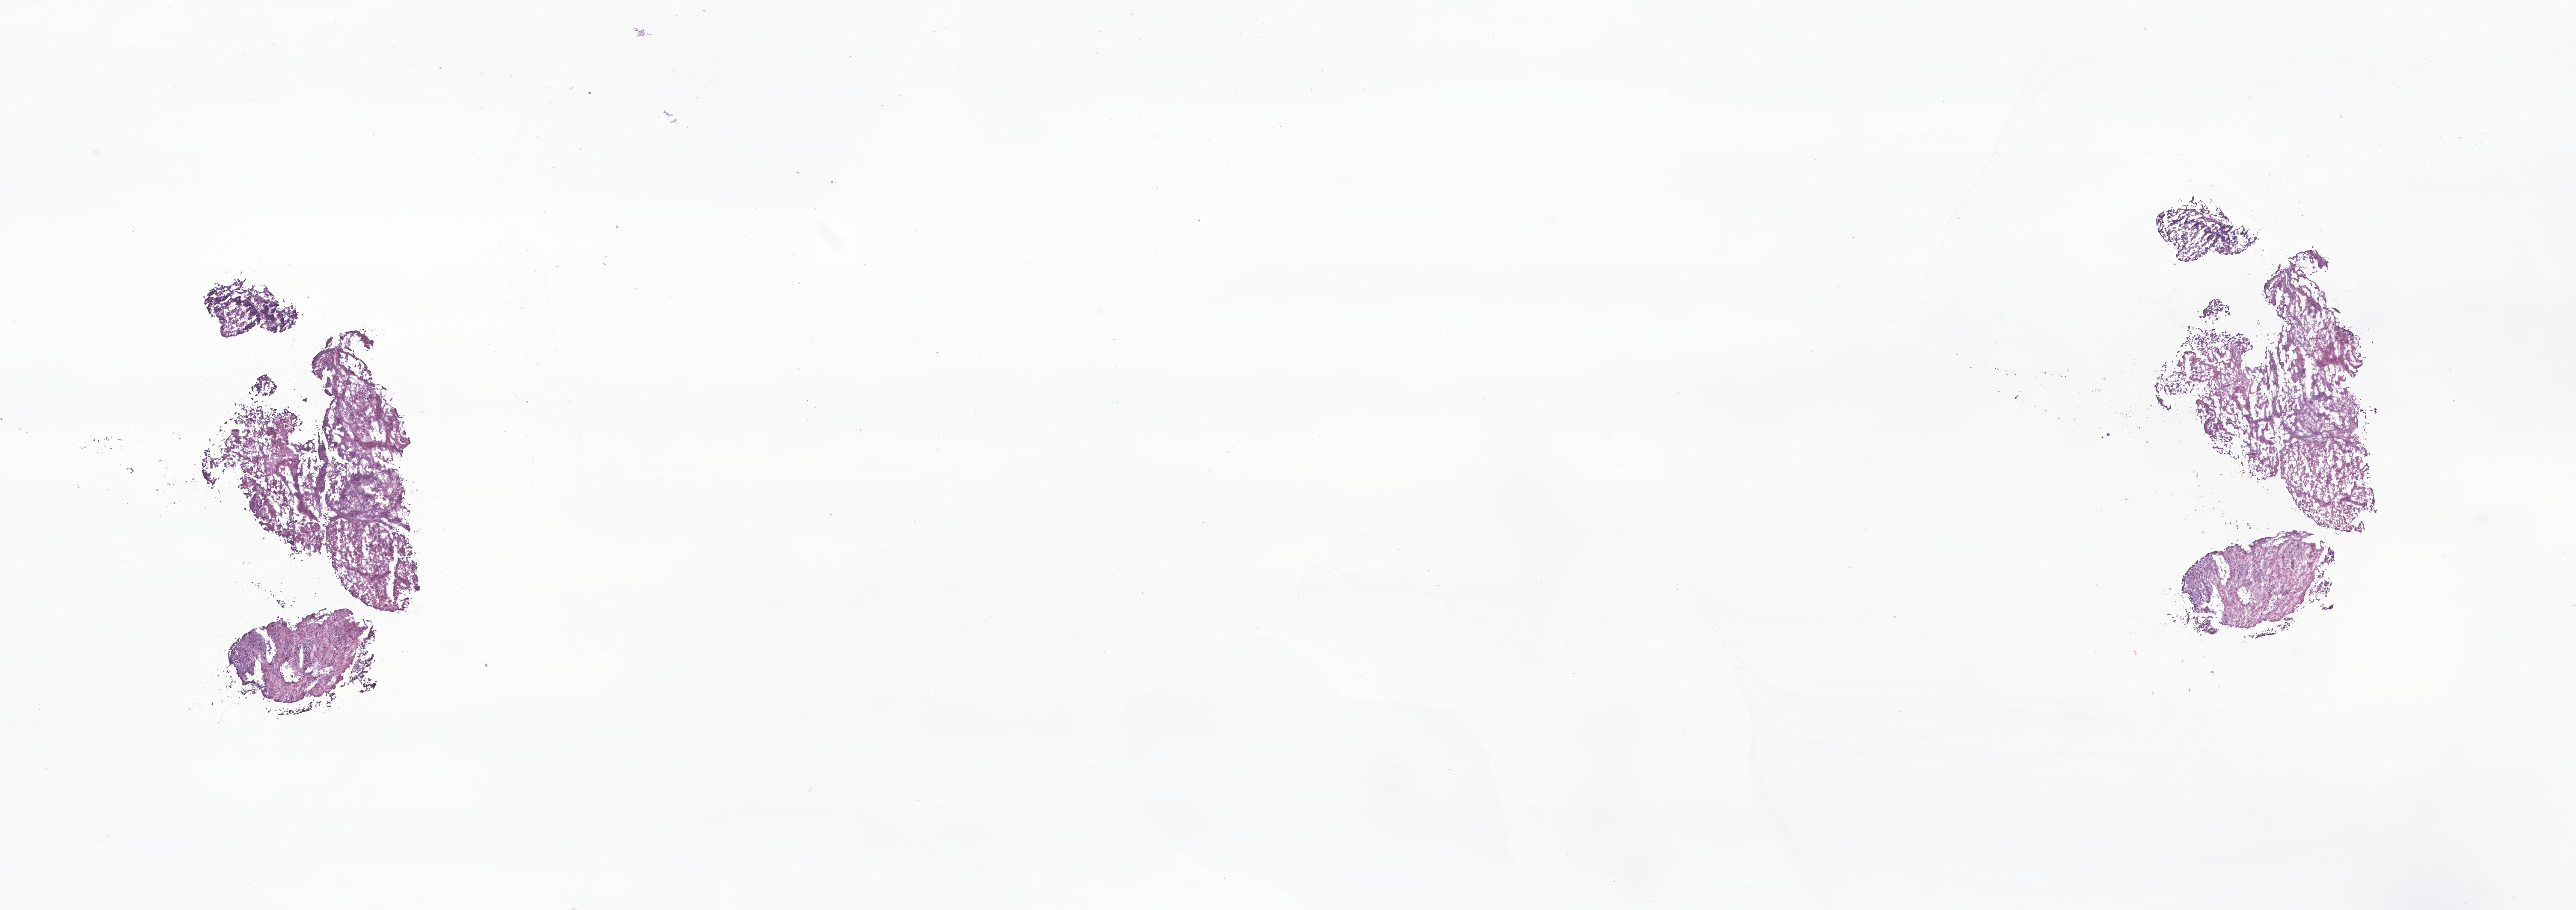
Digitized hematoxylin and eosin (H&E)-stained section of tumor tissue from the kidney, a low-resolution overview of the entire scanned area, about 25.4 x 9.0 mm, frozen section. Patient male; age 816 days (about 2.2 years).
Recorded diagnosis: Rhabdoid tumor, NOS.